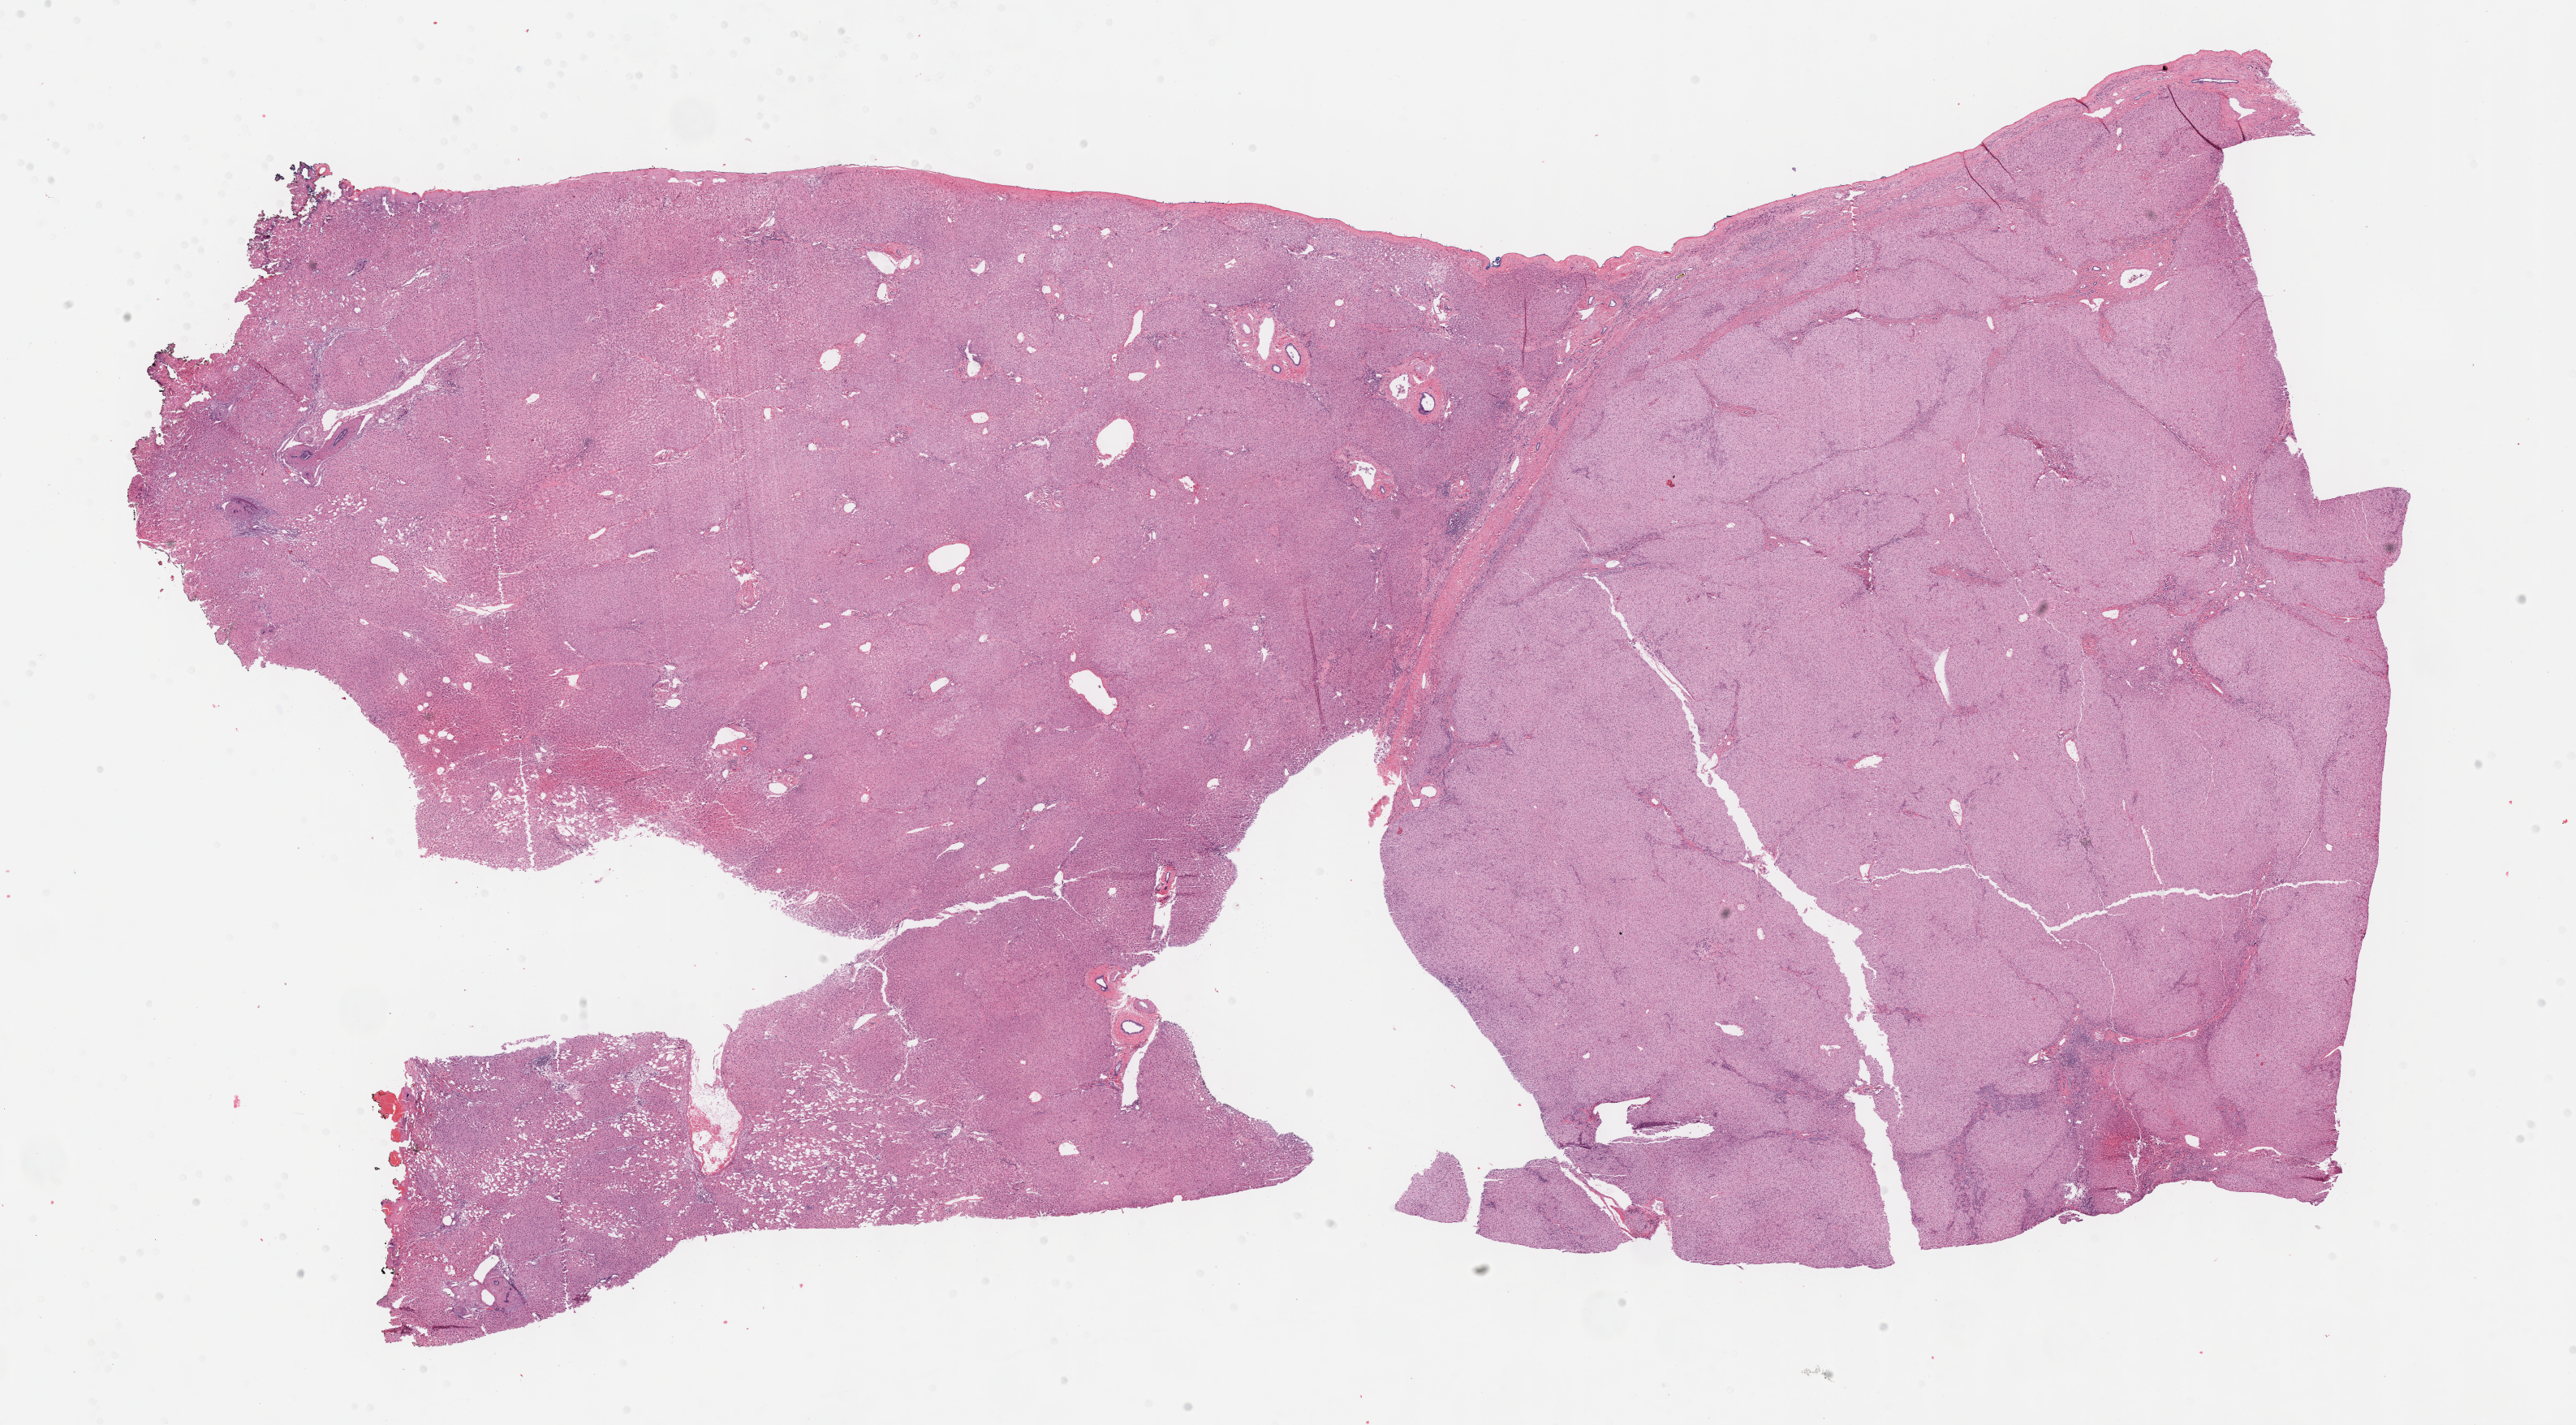
H&E-stained whole-slide image, whole scanned area (about 25.7 x 14.2 mm, acquisition: 40x scan) shown as a low-resolution overview; FFPE section; sample: primary tumour, liver. Female, age 69 years at initial diagnosis. Histologic grade: G1 (well differentiated).
* AJCC pathologic stage: I (7th edition)
* diagnosis: Hepatocellular carcinoma, NOS